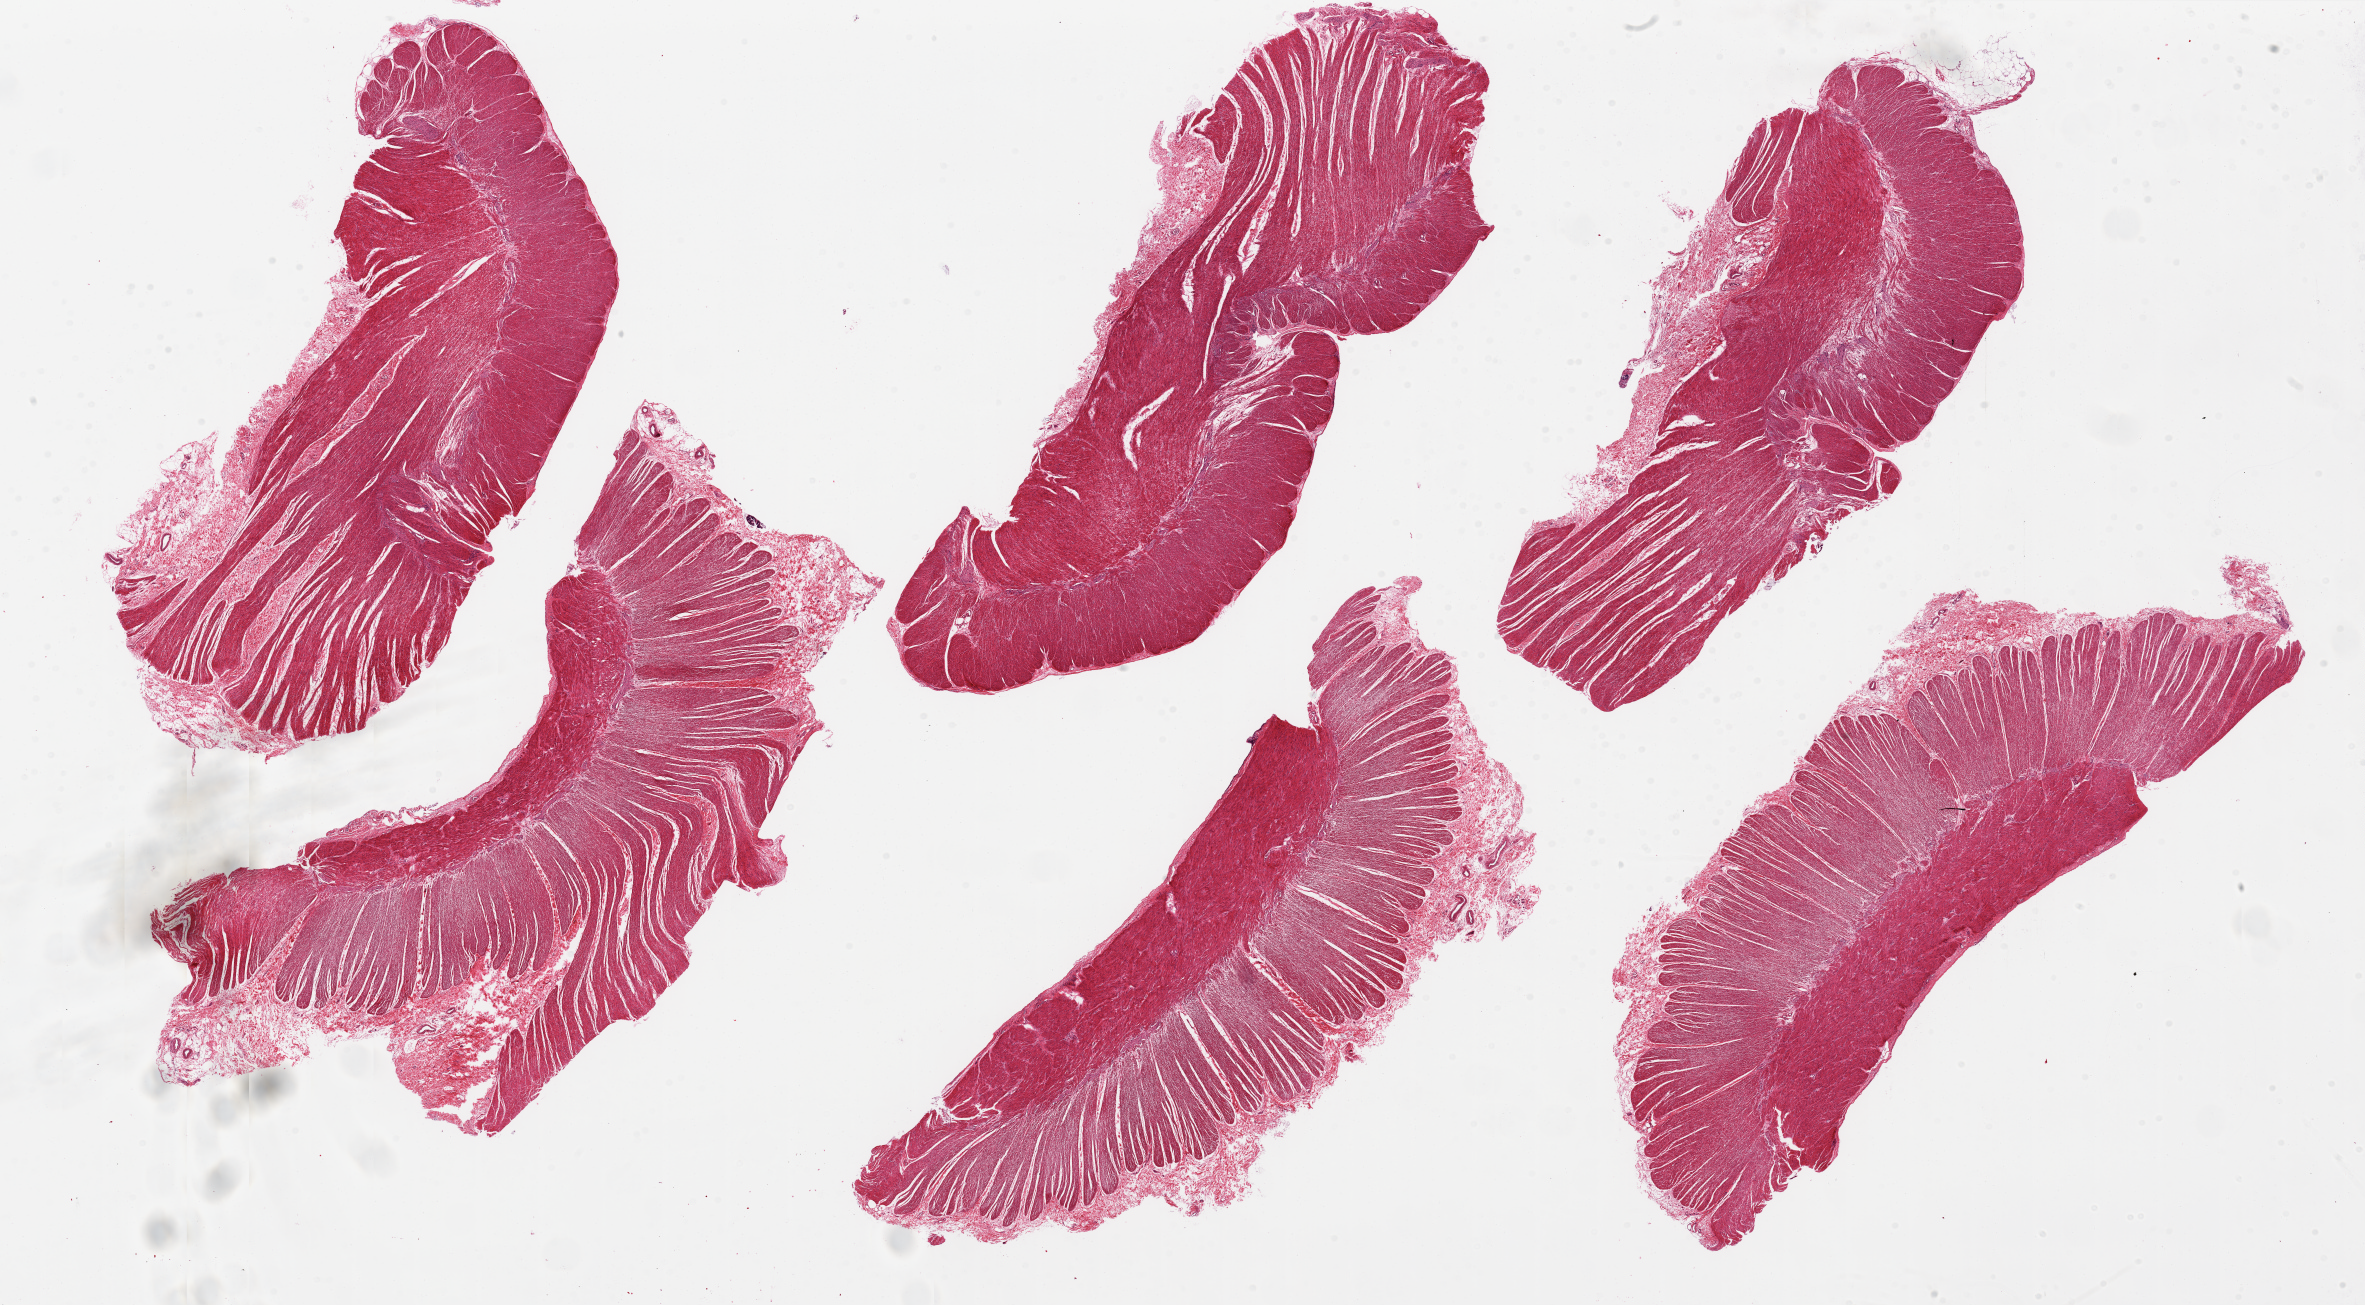
Digitized H&E-stained section, a low-resolution overview of the entire scanned area, about 37.4 x 20.6 mm; PAXgene-fixed, paraffin-embedded tissue; section of sigmoid colon (target tissue); tissue donor sample. Male donor.
Pathologist's review note for this sample: 6 pieces, well trimmed of mucosa.